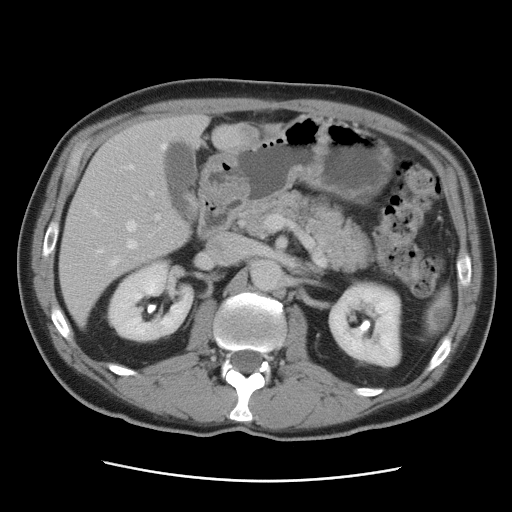
Contrast-enhanced abdominal CT, one axial slice; slice 46 of 89 in the series (ordered by position); 120 kVp; intravenous contrast given; soft-tissue window (W 400 / L 40 HU); 5 mm slice thickness; 512 × 512 image matrix, field of view 366 × 366 mm. Male patient, age 59 years. Case-level facts recorded for this patient, not image findings: diagnosis: colorectal cancer liver metastases, imaged before liver resection; multiple liver metastases: yes.
Annotated regions visible in this slice (outlined manually by an expert reader):
- hepatic veins: bounding box <94,144,166,266> (left, top, right, bottom; pixels)
- liver: <60,116,270,329>
- planned liver remnant (the part of the liver to remain after resection): <71,116,207,245>
- portal vein (with intrahepatic branches): <134,192,160,220>
- liver metastasis: <239,127,260,144>